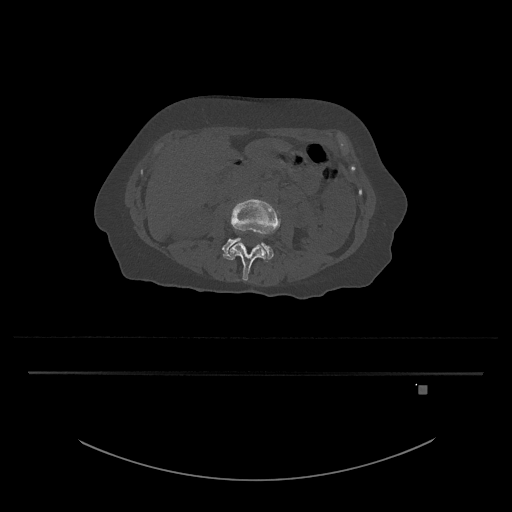
CT including the spine, one axial slice. Slice 406 of 797 in the series (ordered by position). Bone window (W 1800 / L 400 HU). 0.5 mm slice thickness. 512 × 512 image matrix, field of view 500 × 500 mm. Female patient, age 57 years. Case-level facts recorded for this patient, not image findings: primary cancer: cervical.
Outlined on this slice (semi-automatic segmentation, software-assisted and operator-edited):
- L3 vertebra: box from (x=223, y=199) to (x=281, y=281) px
- L4 vertebra: (x=222, y=238)–(x=274, y=262)